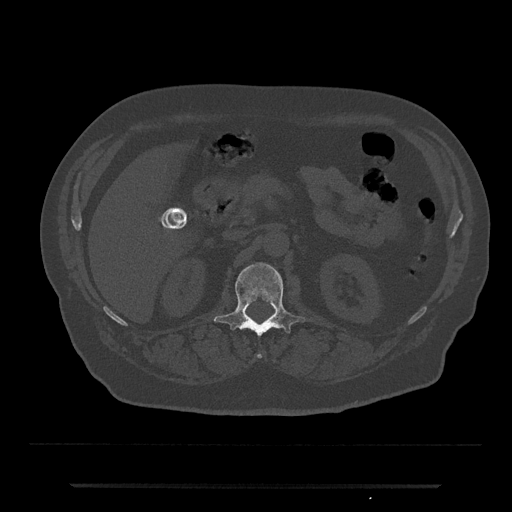
CT including the spine, one axial slice. Position 538 of 797 along the scan axis. 120 kVp. Bone window (W 1800 / L 400 HU). 512 × 512 image matrix, field of view 434 × 434 mm. Patient: male, 80 years. Case-level facts recorded for this patient, not image findings: primary cancer: prostate.
Annotated regions visible in this slice (semi-automatic segmentation, software-assisted and operator-edited):
- L1 vertebra: bounding box (x1, y1, x2, y2) in pixels: (214, 262, 305, 359)